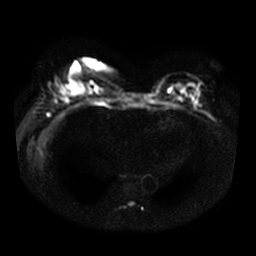
Breast MRI, one axial slice. Slice 16 of 34 in the series (ordered by position). Diffusion-weighted series; image 2 of 4 stored at this slice position (different b-values; order by instance number). 3 T. 5 mm slice thickness. 256 × 256 image matrix, field of view 330 × 330 mm. Female patient.
Annotated regions visible in this slice (outlined manually by an expert reader):
- tumour on diffusion-weighted imaging: box from (x=67, y=80) to (x=81, y=91) px